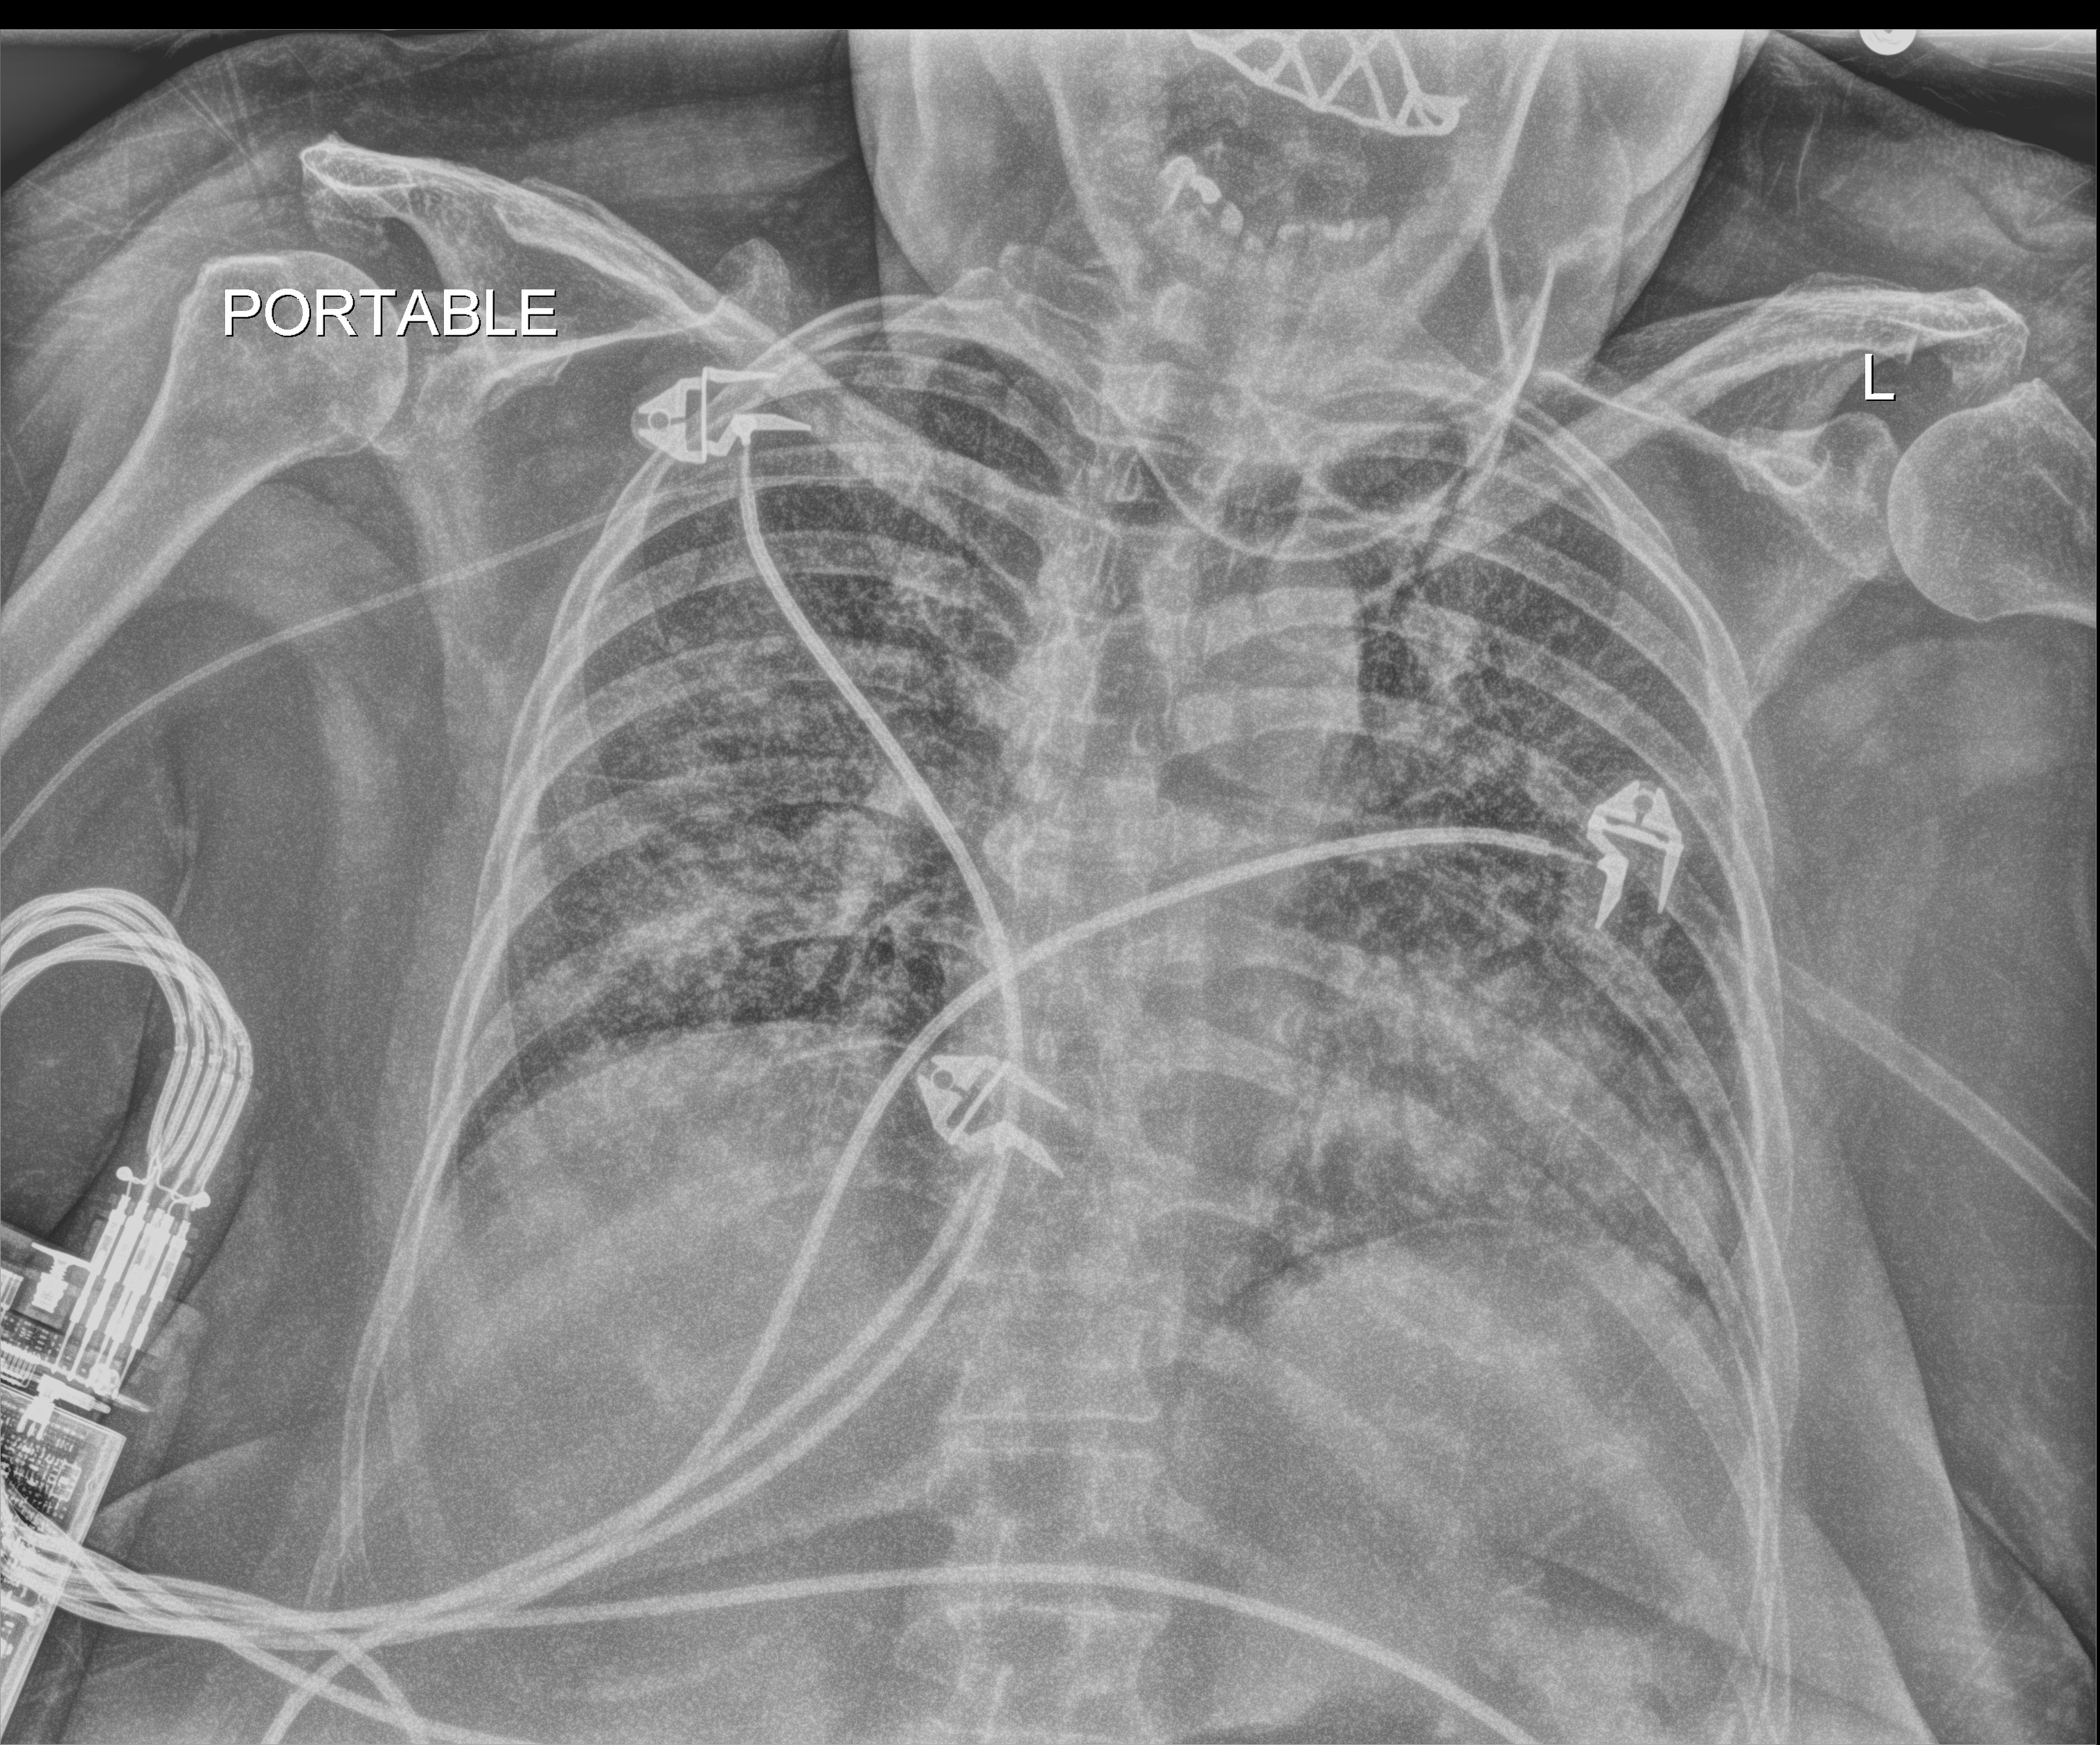
Bedside chest radiograph (digital radiography). Patient hospitalised with COVID-19; female, aged 60–74 years.
From the hospital-stay record, not from the radiograph (when in the stay this image was taken is not recorded):
- admitted to intensive care during this hospital stay: yes